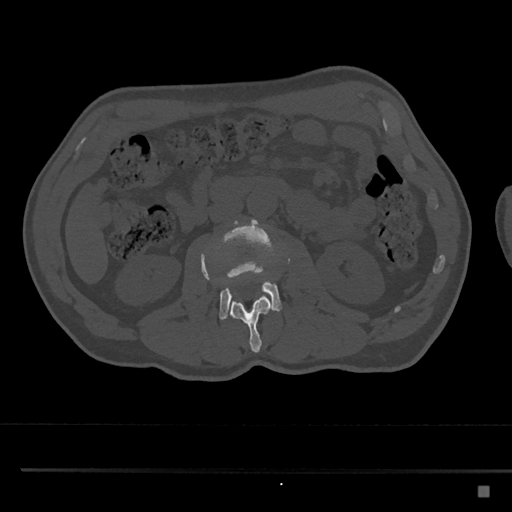
CT including the spine, one axial slice; position 730 of 797 along the scan axis; 120 kVp; bone window (W 1800 / L 400 HU); 0.5 mm slice thickness; 512 × 512 image matrix, field of view 391 × 391 mm. Male patient, age 59 years. From the clinical record (not read from this slice): primary cancer: prostate.
Annotated regions visible in this slice (semi-automatic segmentation, software-assisted and operator-edited):
- L2 vertebra: bounding box [x1, y1, x2, y2] px = [201, 254, 272, 353]
- L3 vertebra: [201, 219, 290, 320]